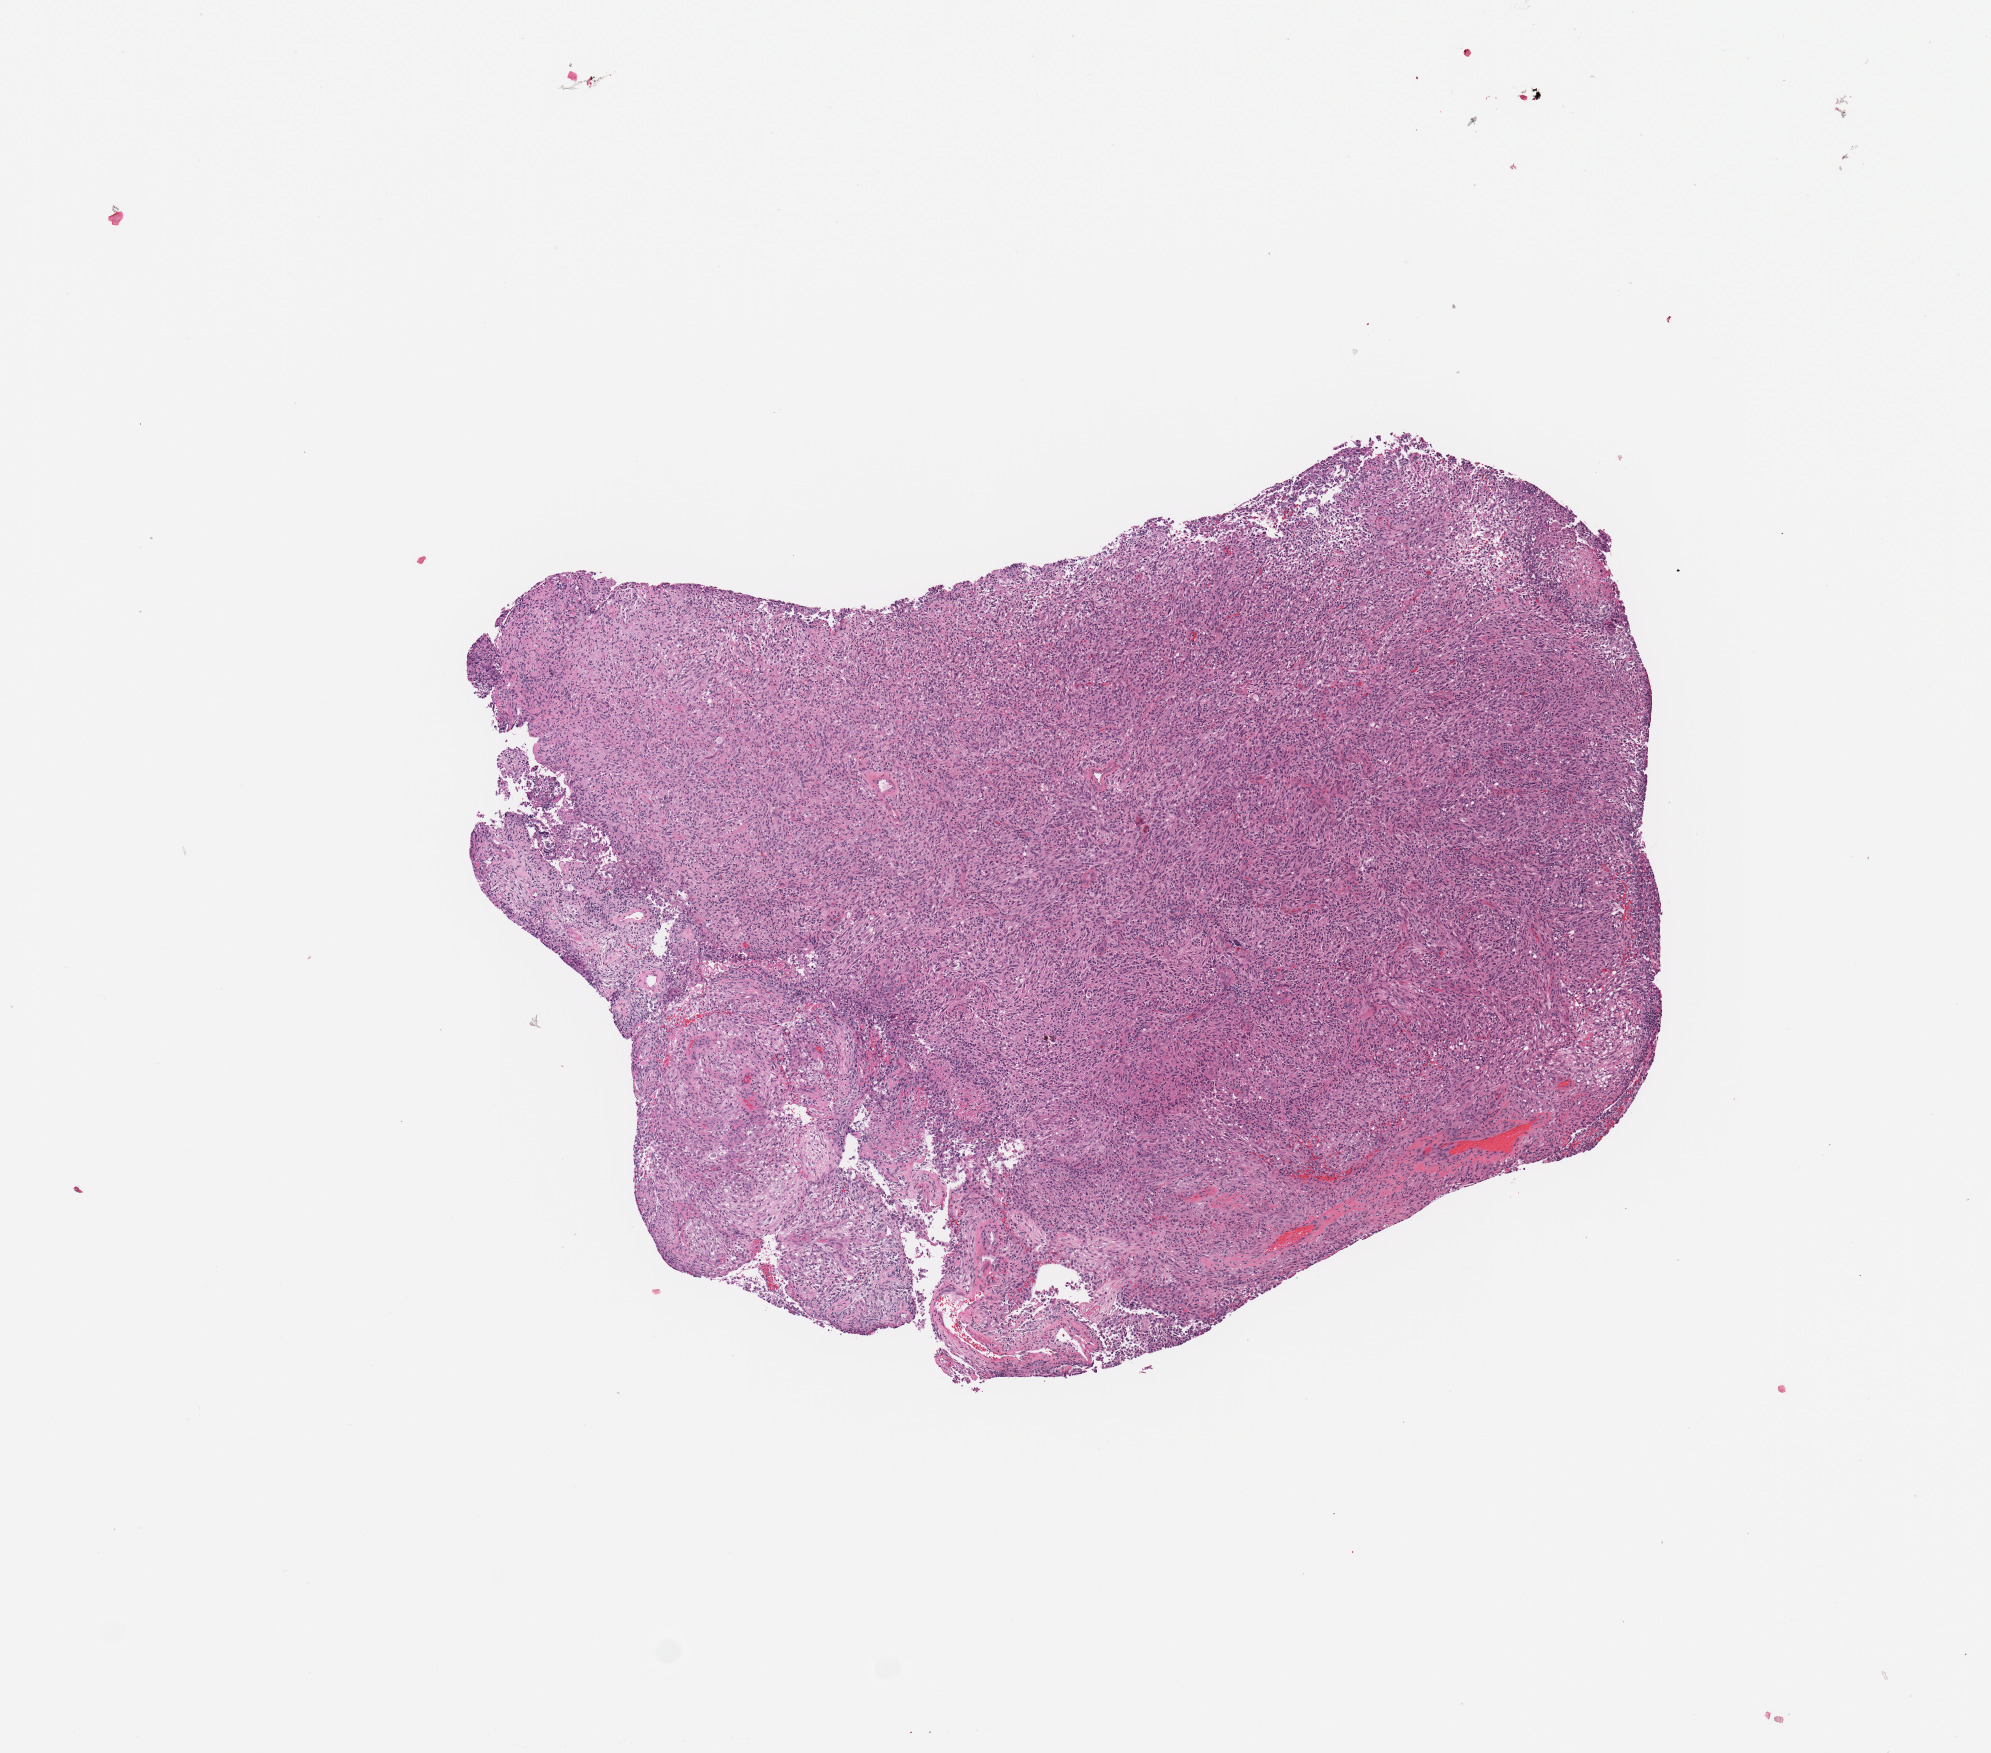
Whole-slide histology image, H&E-stained, whole scanned area (about 7.9 x 6.9 mm, acquisition: 20x scan) shown as a low-resolution overview; tumour tissue sample, sampled site: frontal lobe. Female, 42 y/o. Pathologist review of this section (percent, as recorded): tumour nuclei 90%, necrosis 3%.
Diagnosis: Glioblastoma.